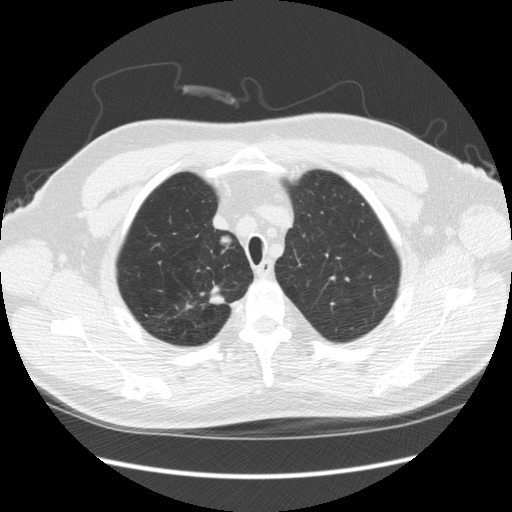
Low-dose screening chest CT, axial slice; third annual screen; lung window (W 1500 / L -600 HU); 2.5 mm slice thickness; slice 35 of 248 in the series; 512 × 512 image matrix, field of view 380 × 380 mm. Male participant, aged 64 years at enrolment. Former smoker at enrolment.
2 expert-annotated lung lesions on this slice (largest first), box from (x=201, y=230) to (x=242, y=259) px; (x=199, y=281)–(x=232, y=313). The screening reader recorded 4 non-calcified nodules or masses ≥4 mm on this exam; which of them these boxes mark is not recorded. Official screen result: positive, other.